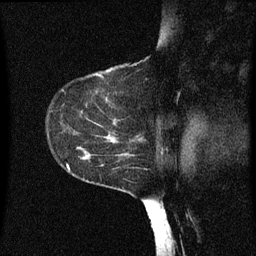
Breast MRI (dynamic contrast-enhanced), one sagittal slice; slice 45 of 60 in the series (ordered by position); dynamic contrast-enhanced series, image 2 of 3 at this slice position (ordered by acquisition); 1.5 T; TE 4.2 ms, TR 8 ms; 256 × 256 image matrix, field of view 200 × 200 mm. Female patient, age 55 years.
Annotated regions visible in this slice (semi-automatic segmentation, software-assisted and operator-edited):
- analysis volume of interest (the breast-tissue region the enhancement analysis was run in; not a lesion): bounding box (x1, y1, x2, y2) in pixels: (46, 124, 151, 183)
- tumour enhancement mask (voxels above the 70 % enhancement threshold inside the analysis volume of interest): (76, 136, 139, 157)